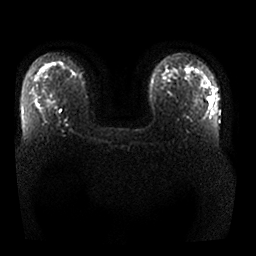
Breast MRI, one axial slice; slice 18 of 25 in the series (ordered by position); diffusion-weighted series; image 2 of 4 stored at this slice position (different b-values; order by instance number); 1.5 T; 256 × 256 image matrix, field of view 360 × 360 mm. Female patient.
Annotated regions visible in this slice (manually delineated by an expert):
- tumour on diffusion-weighted imaging: bounding box (x1, y1, x2, y2) in pixels: (208, 97, 213, 102)